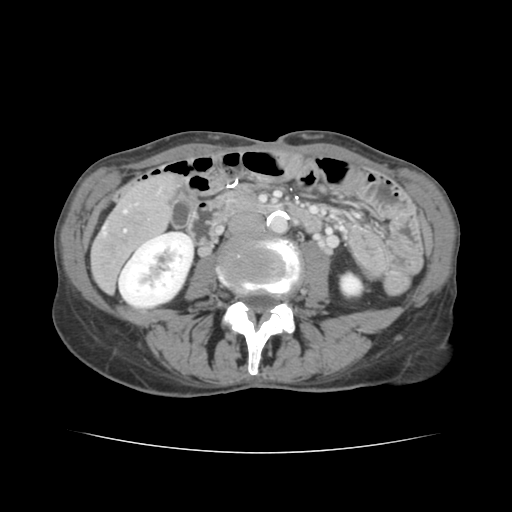
Contrast-enhanced abdominal CT, one axial slice; slice 35 of 136 in the series (ordered by position); 120 kVp; intravenous contrast given; soft-tissue window (W 400 / L 40 HU); 512 × 512 image matrix. Female patient, age 77 years. Case-level facts recorded for this patient, not image findings: diagnosis: colorectal cancer liver metastases, imaged before liver resection; multiple liver metastases: yes; largest metastasis: 3 cm; disease in both lobes: no.
Structures marked on this image (manually delineated by an expert):
- hepatic veins: bounding box (x1, y1, x2, y2) in pixels: (104, 211, 126, 234)
- liver: (92, 176, 176, 289)